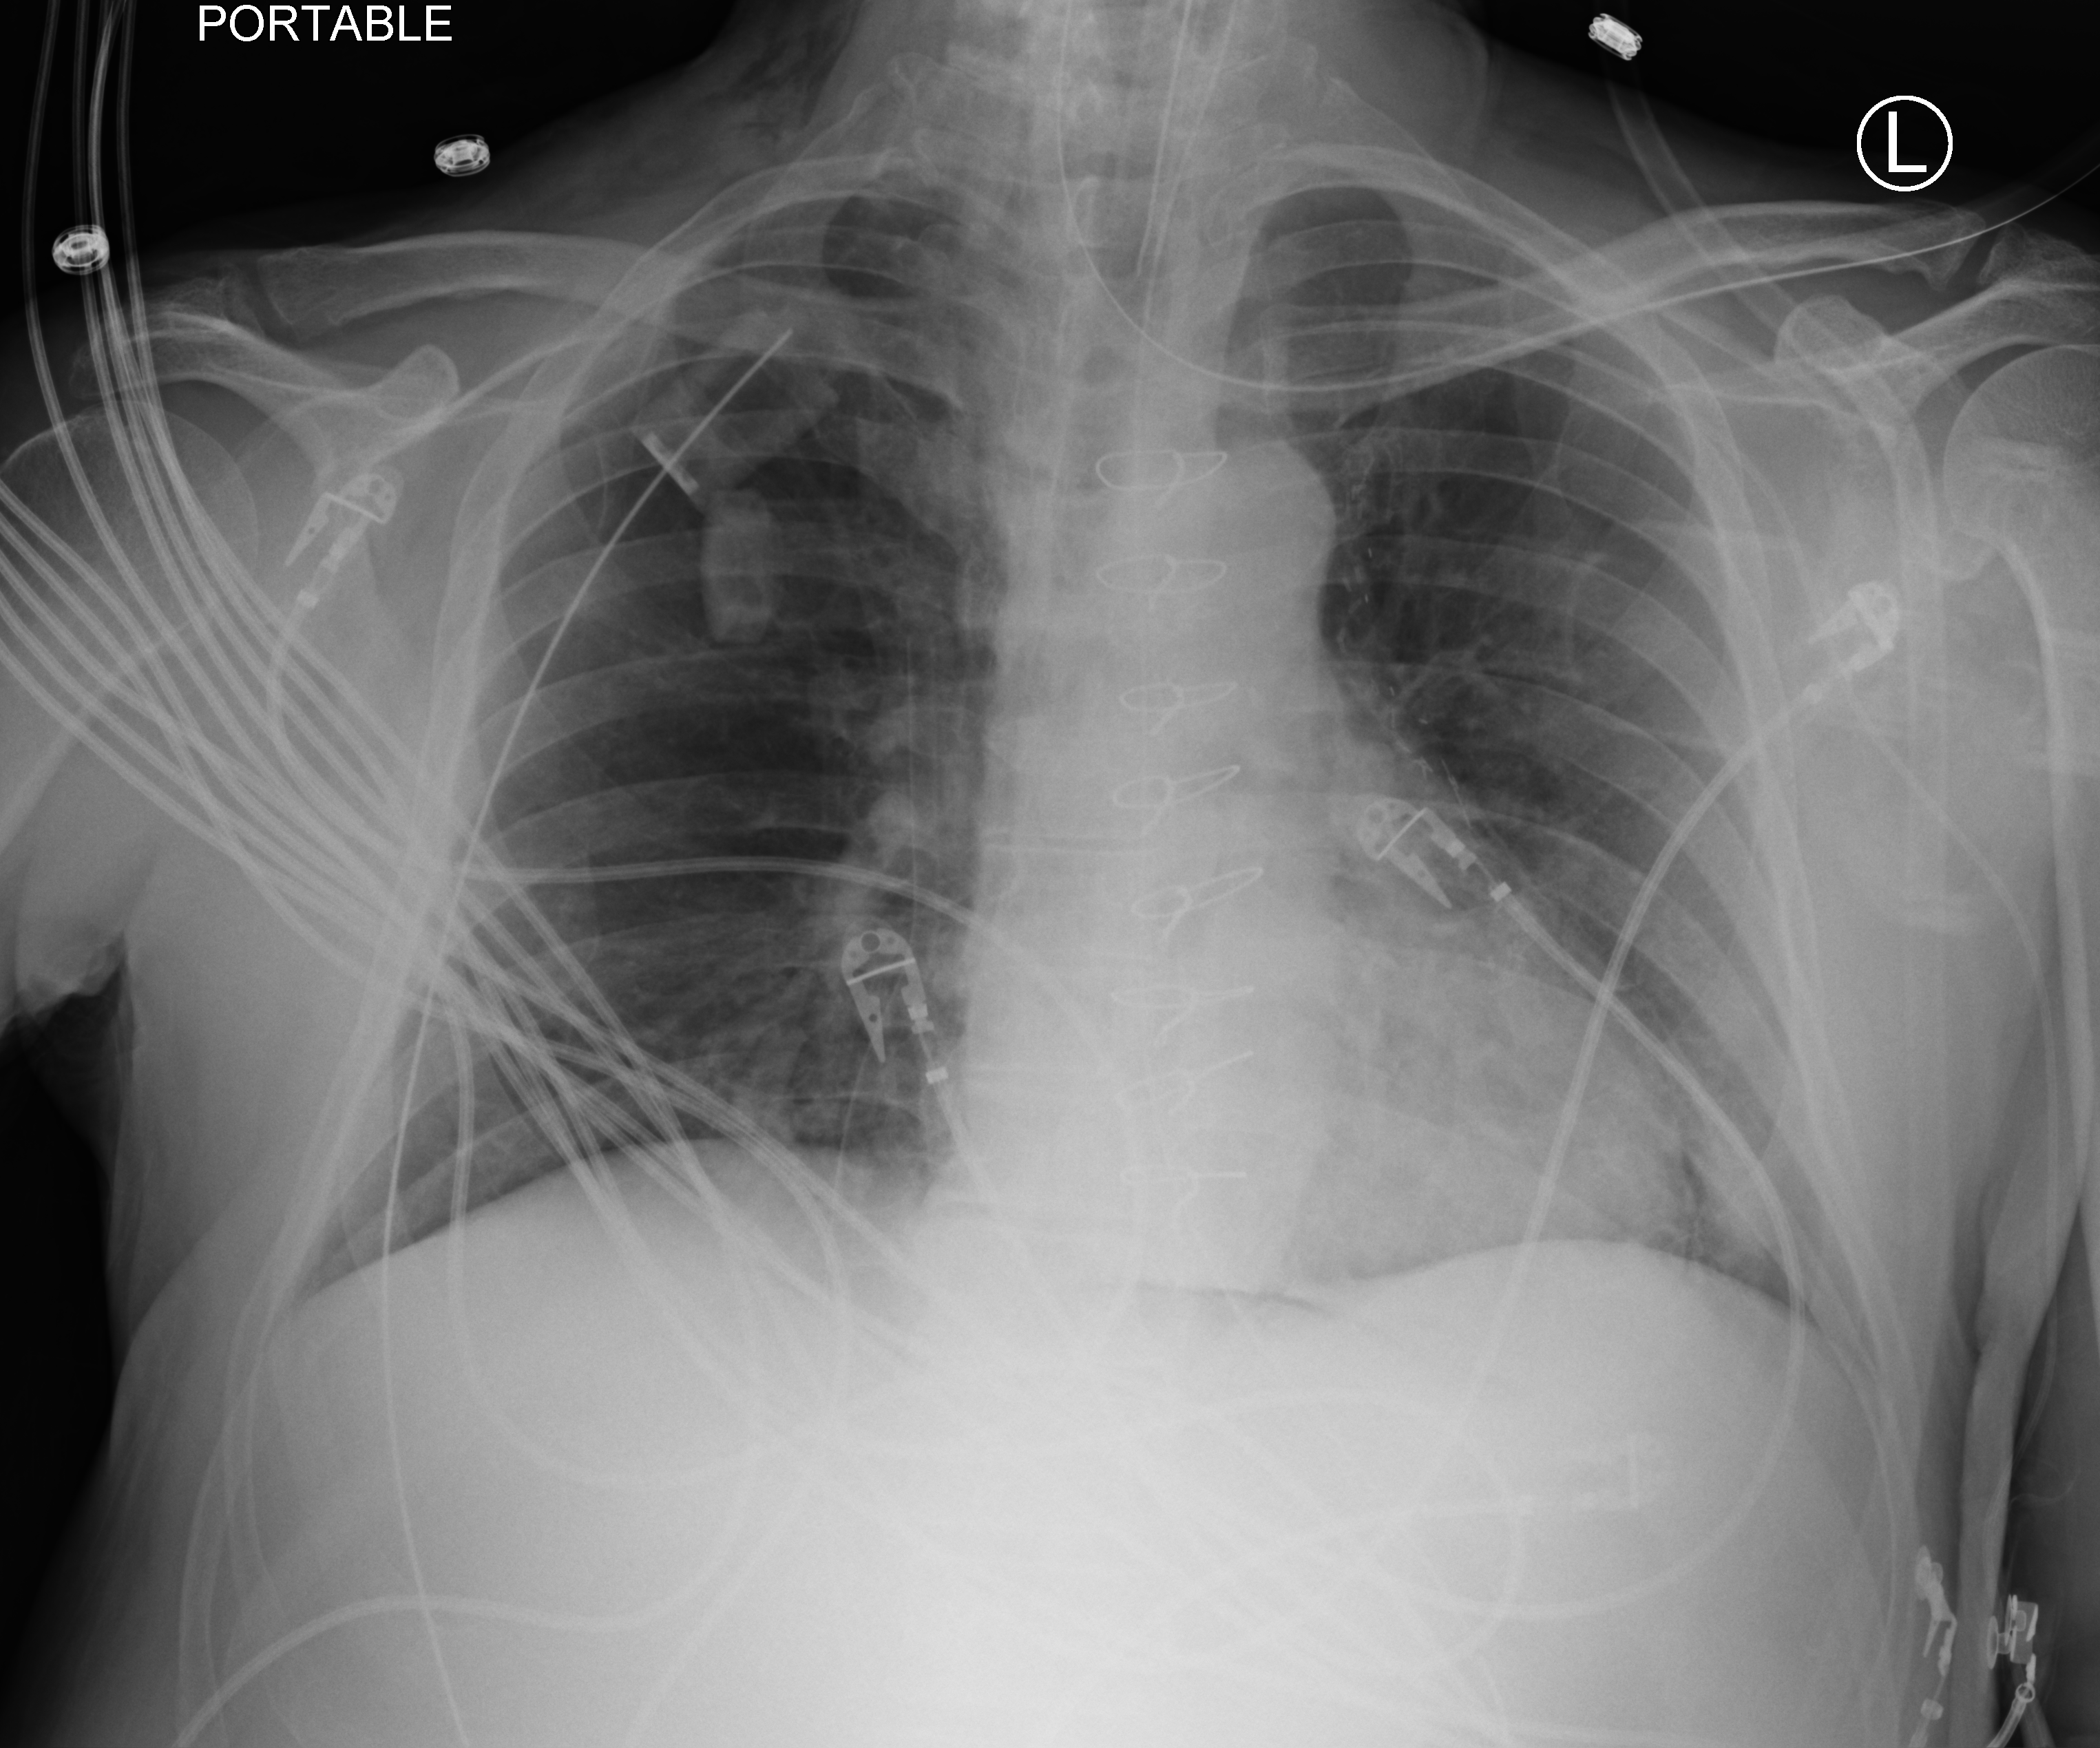
Bedside chest radiograph (computed radiography); anteroposterior (AP) projection. Male patient hospitalised with COVID-19, age 60–74 years.
From the hospital-stay record, not from the radiograph (when in the stay this image was taken is not recorded): mechanically ventilated during this hospital stay: yes.